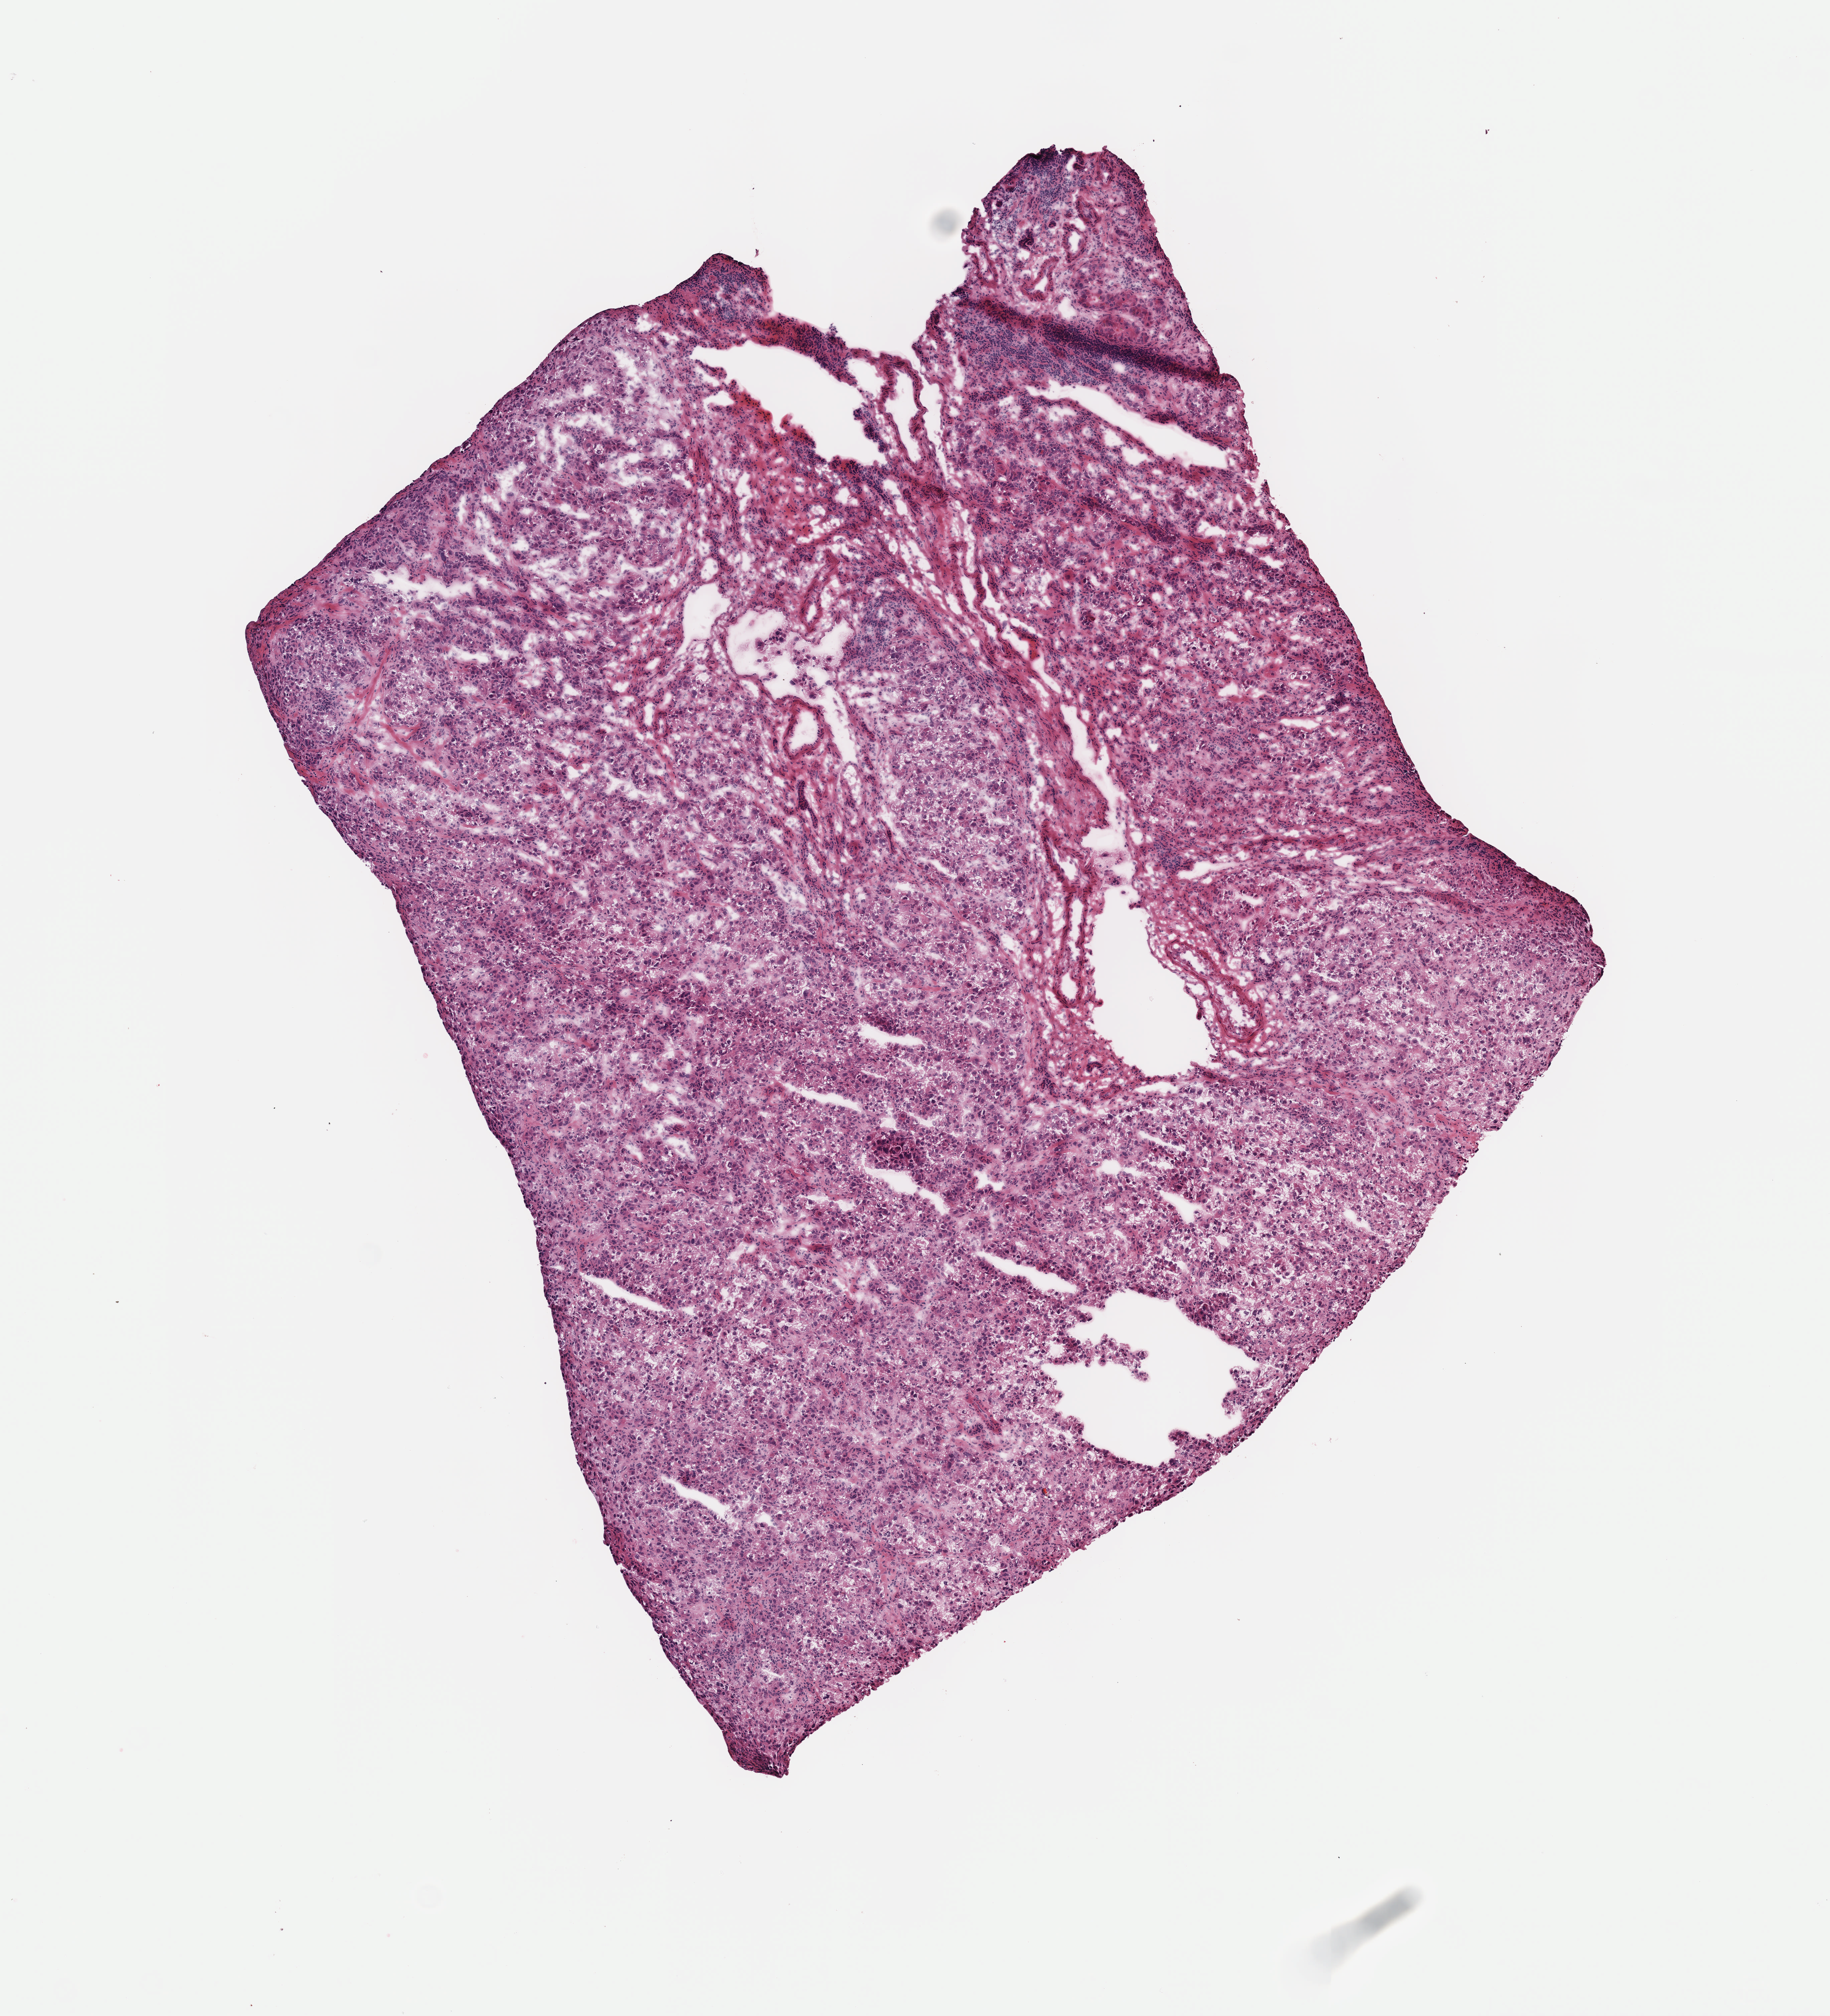
Digitized H&E-stained tissue section (whole slide) — shown as a low-resolution overview of the whole scanned area (about 5.5 x 6.1 mm). Frozen section. Liver, primary tumour sample. Patient: female, age at initial diagnosis 51 years. Histologic grade: G4 (undifferentiated). Composition of this section per pathologist review: tumour cells 90%, tumour nuclei 95%, normal cells 0%, stromal cells 10%, necrosis 0%. Infiltration values recorded for this section: lymphocyte infiltration 0%, monocyte infiltration 0%, neutrophil infiltration 0%.
AJCC pathologic stage: I. Diagnosis: Hepatocellular carcinoma, NOS.